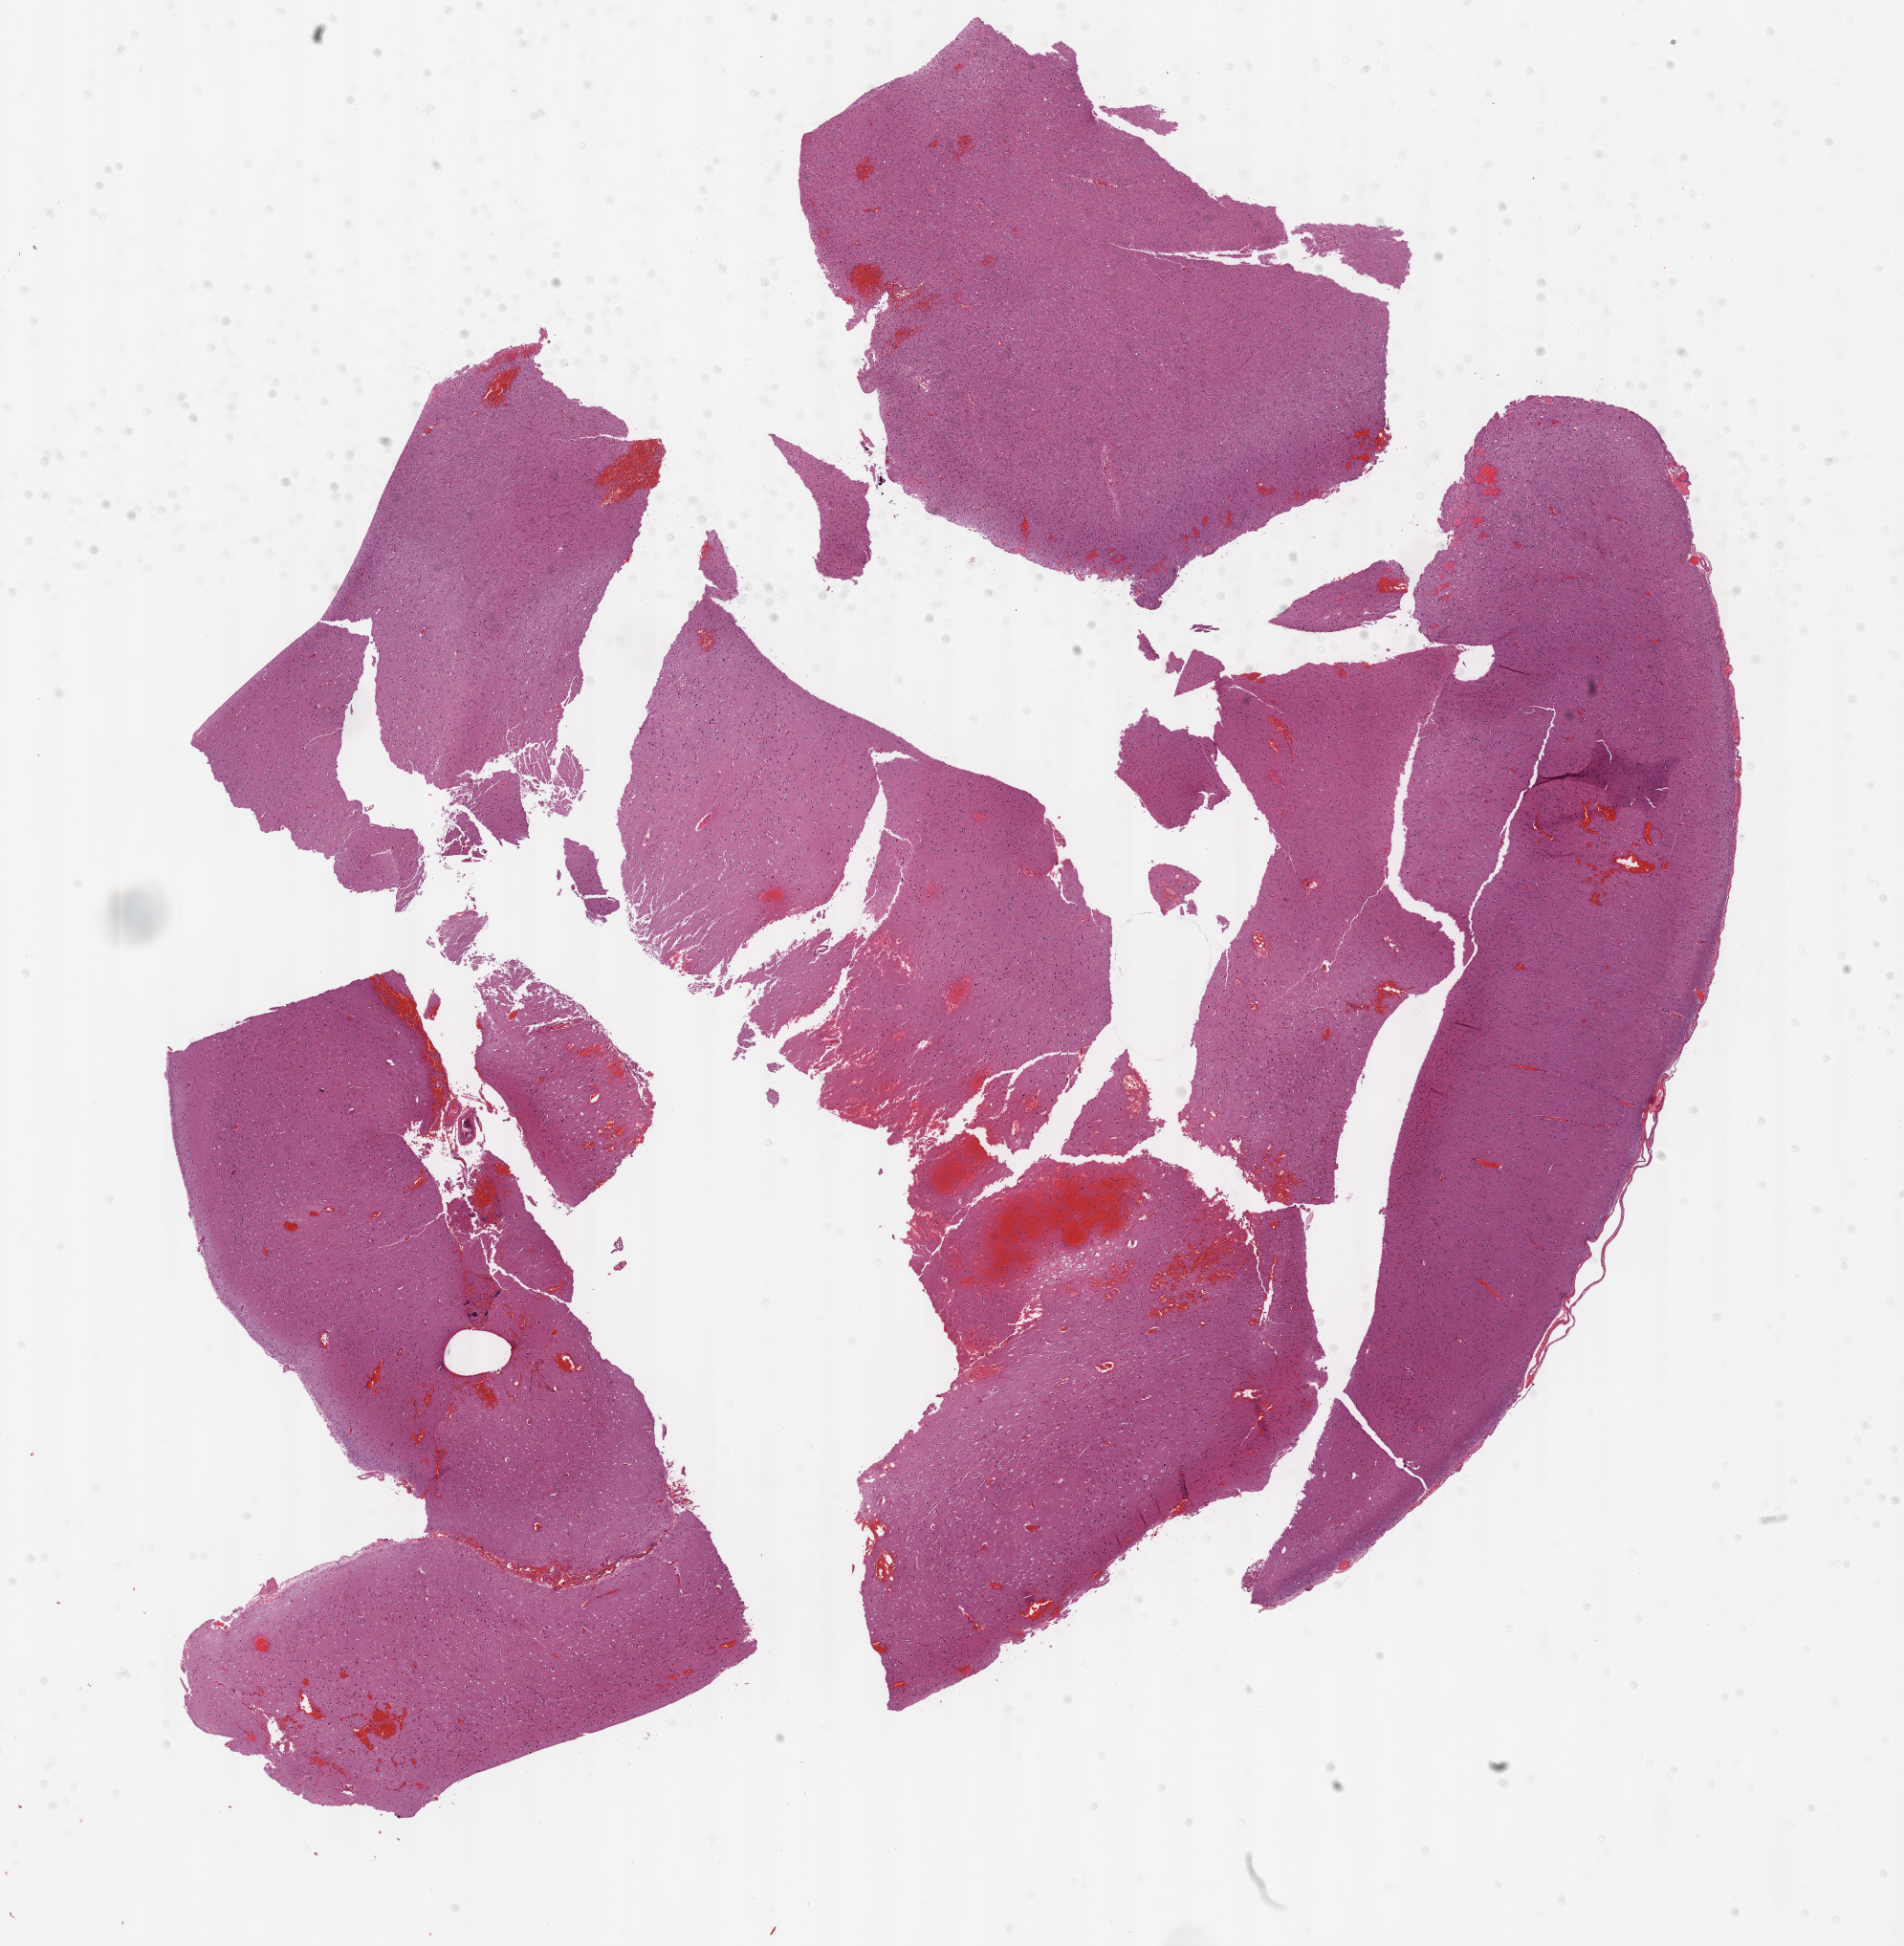
Hematoxylin and eosin (H&E) stained whole-slide image — low-resolution overview of the scanned area, about 16.1 x 16.5 mm, formalin-fixed paraffin-embedded (FFPE) diagnostic section, sample: primary tumour, brain. Male patient; age at initial diagnosis 37 years. Histologic grade: G3 (poorly differentiated).
Histologic diagnosis: Oligodendroglioma, anaplastic.